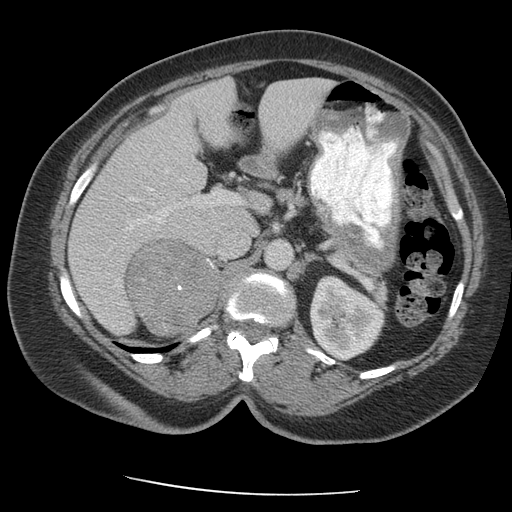
Contrast-enhanced abdominal CT, one axial slice. Position 124 of 163 along the scan axis. Reconstruction kernel STANDARD. 140 kVp. Intravenous contrast given. Soft-tissue window (W 400 / L 40 HU). 512 × 512 image matrix, field of view 360 × 360 mm. Patient: female, 70 years. Case-level facts recorded for this patient, not image findings: diagnosis: adrenocortical carcinoma; tumour side: right adrenal.
Structures marked on this image (semi-automatic segmentation, software-assisted and operator-edited):
- mass: bounding box <127,240,216,336> (left, top, right, bottom; pixels)